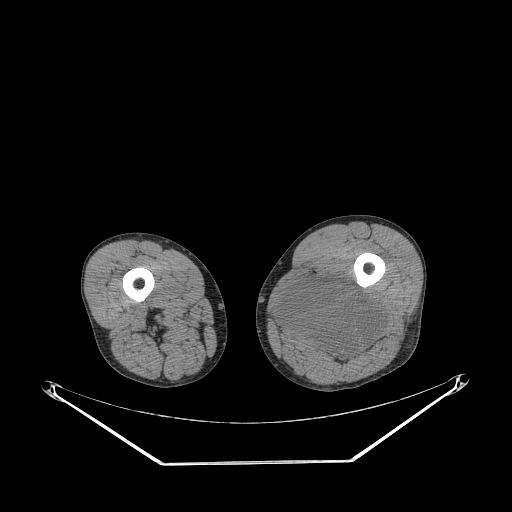
CT of an extremity soft-tissue mass (from a PET/CT study), one axial slice; slice 228 of 267 in the series (ordered by position); reconstruction kernel STANDARD; soft-tissue window (W 400 / L 40 HU); 512 × 512 image matrix, field of view 500 × 500 mm. Male patient. From the clinical record (not read from this slice): histological type: undifferentiated pleomorphic liposarcoma; grade: high; site of the primary tumour: left thigh.
Outlined on this slice (expert contour drawn on MRI and transferred to this co-registered scan by the dataset authors):
- gross tumour volume including surrounding oedema: box from (x=274, y=276) to (x=384, y=362) px
- gross tumour volume (mass): (x=276, y=276)–(x=384, y=362)